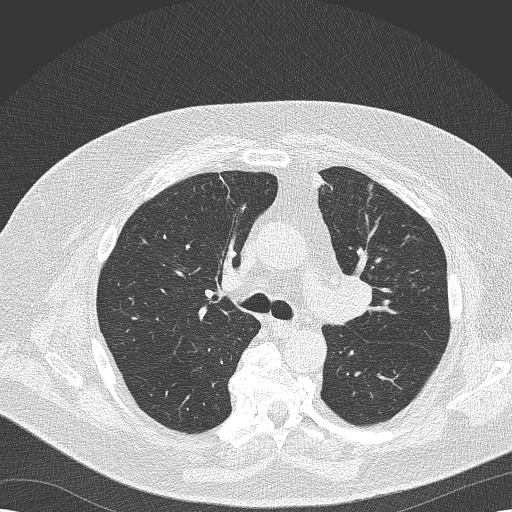
Axial slice from a low-dose chest CT screening exam. Second annual screen. Lung window (W 1500 / L -600 HU). 2 mm slice thickness. Slice 64 of 173 in the series. 512 × 512 image matrix, field of view 370 × 370 mm. Male, age 68 years at enrolment. Former smoker at enrolment.
Expert reader's lesion annotation, bounding box <322,268,376,332> (left, top, right, bottom; pixels). The exam's reader record, not a measurement of the box and not confirmed to be the same lesion: non-calcified nodule or mass ≥4 mm, left lower lobe, 8 × 6 mm, soft tissue attenuation, pre-existing on the prior screen: yes; interval growth: no. Lung cancer was diagnosed 256 days after this screen: squamous cell carcinoma, NOS, left upper lobe, poorly differentiated (G3), stage IIB (AJCC 6th edition), 35 mm at pathology.